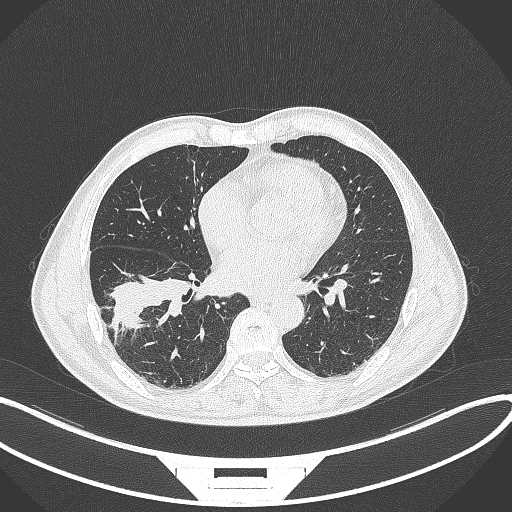
Chest CT, one axial slice. Reconstruction kernel B70f. 120 kVp. Lung window (W 1500 / L -600 HU). 512 × 512 image matrix, field of view 400 × 400 mm. Male patient, age 58 years. From the clinical record (not read from this slice): clinical TNM (as recorded): T3 N0 M0; histopathological grade: G2.
Annotated regions visible in this slice (bounding box drawn by a radiologist):
- lung tumour (recorded histology: squamous cell carcinoma): bounding box <107,277,191,331> (left, top, right, bottom; pixels)